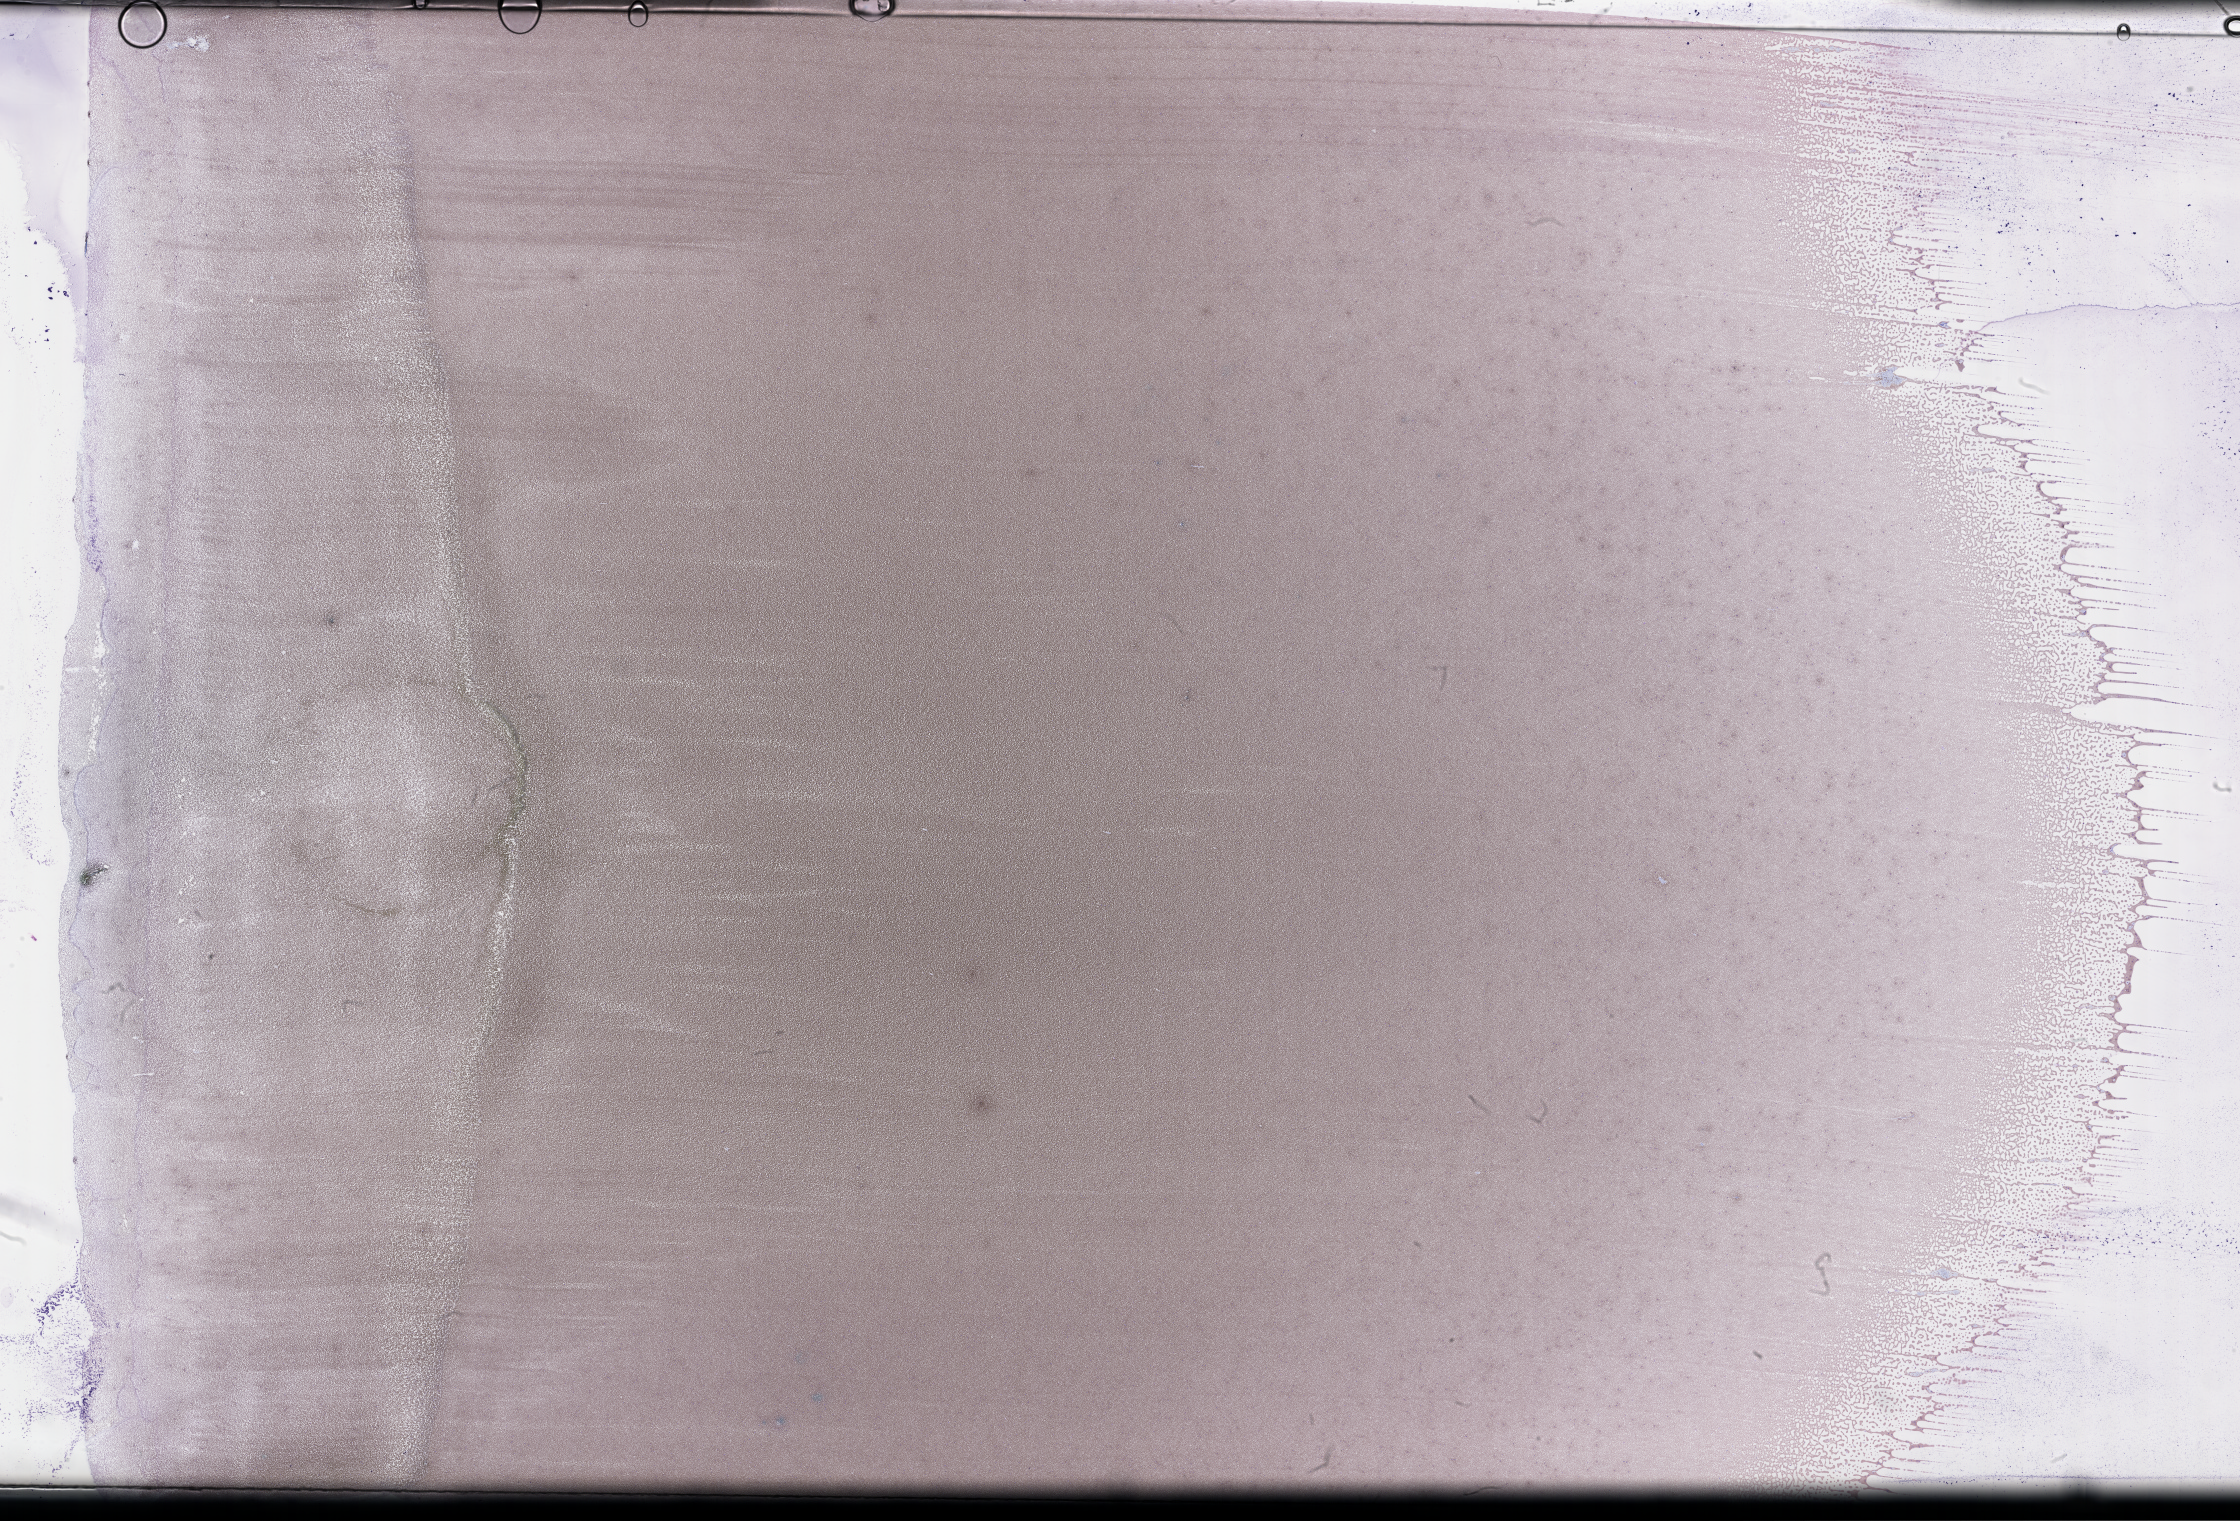
Whole-slide image of a whole blood smear, Wright-Giemsa stain, a low-resolution overview of the entire scanned area, about 36.2 x 24.6 mm; smear from an EDTA sample; collected on treatment. Patient: female.
* patient diagnosis: Plasma Cell Myeloma